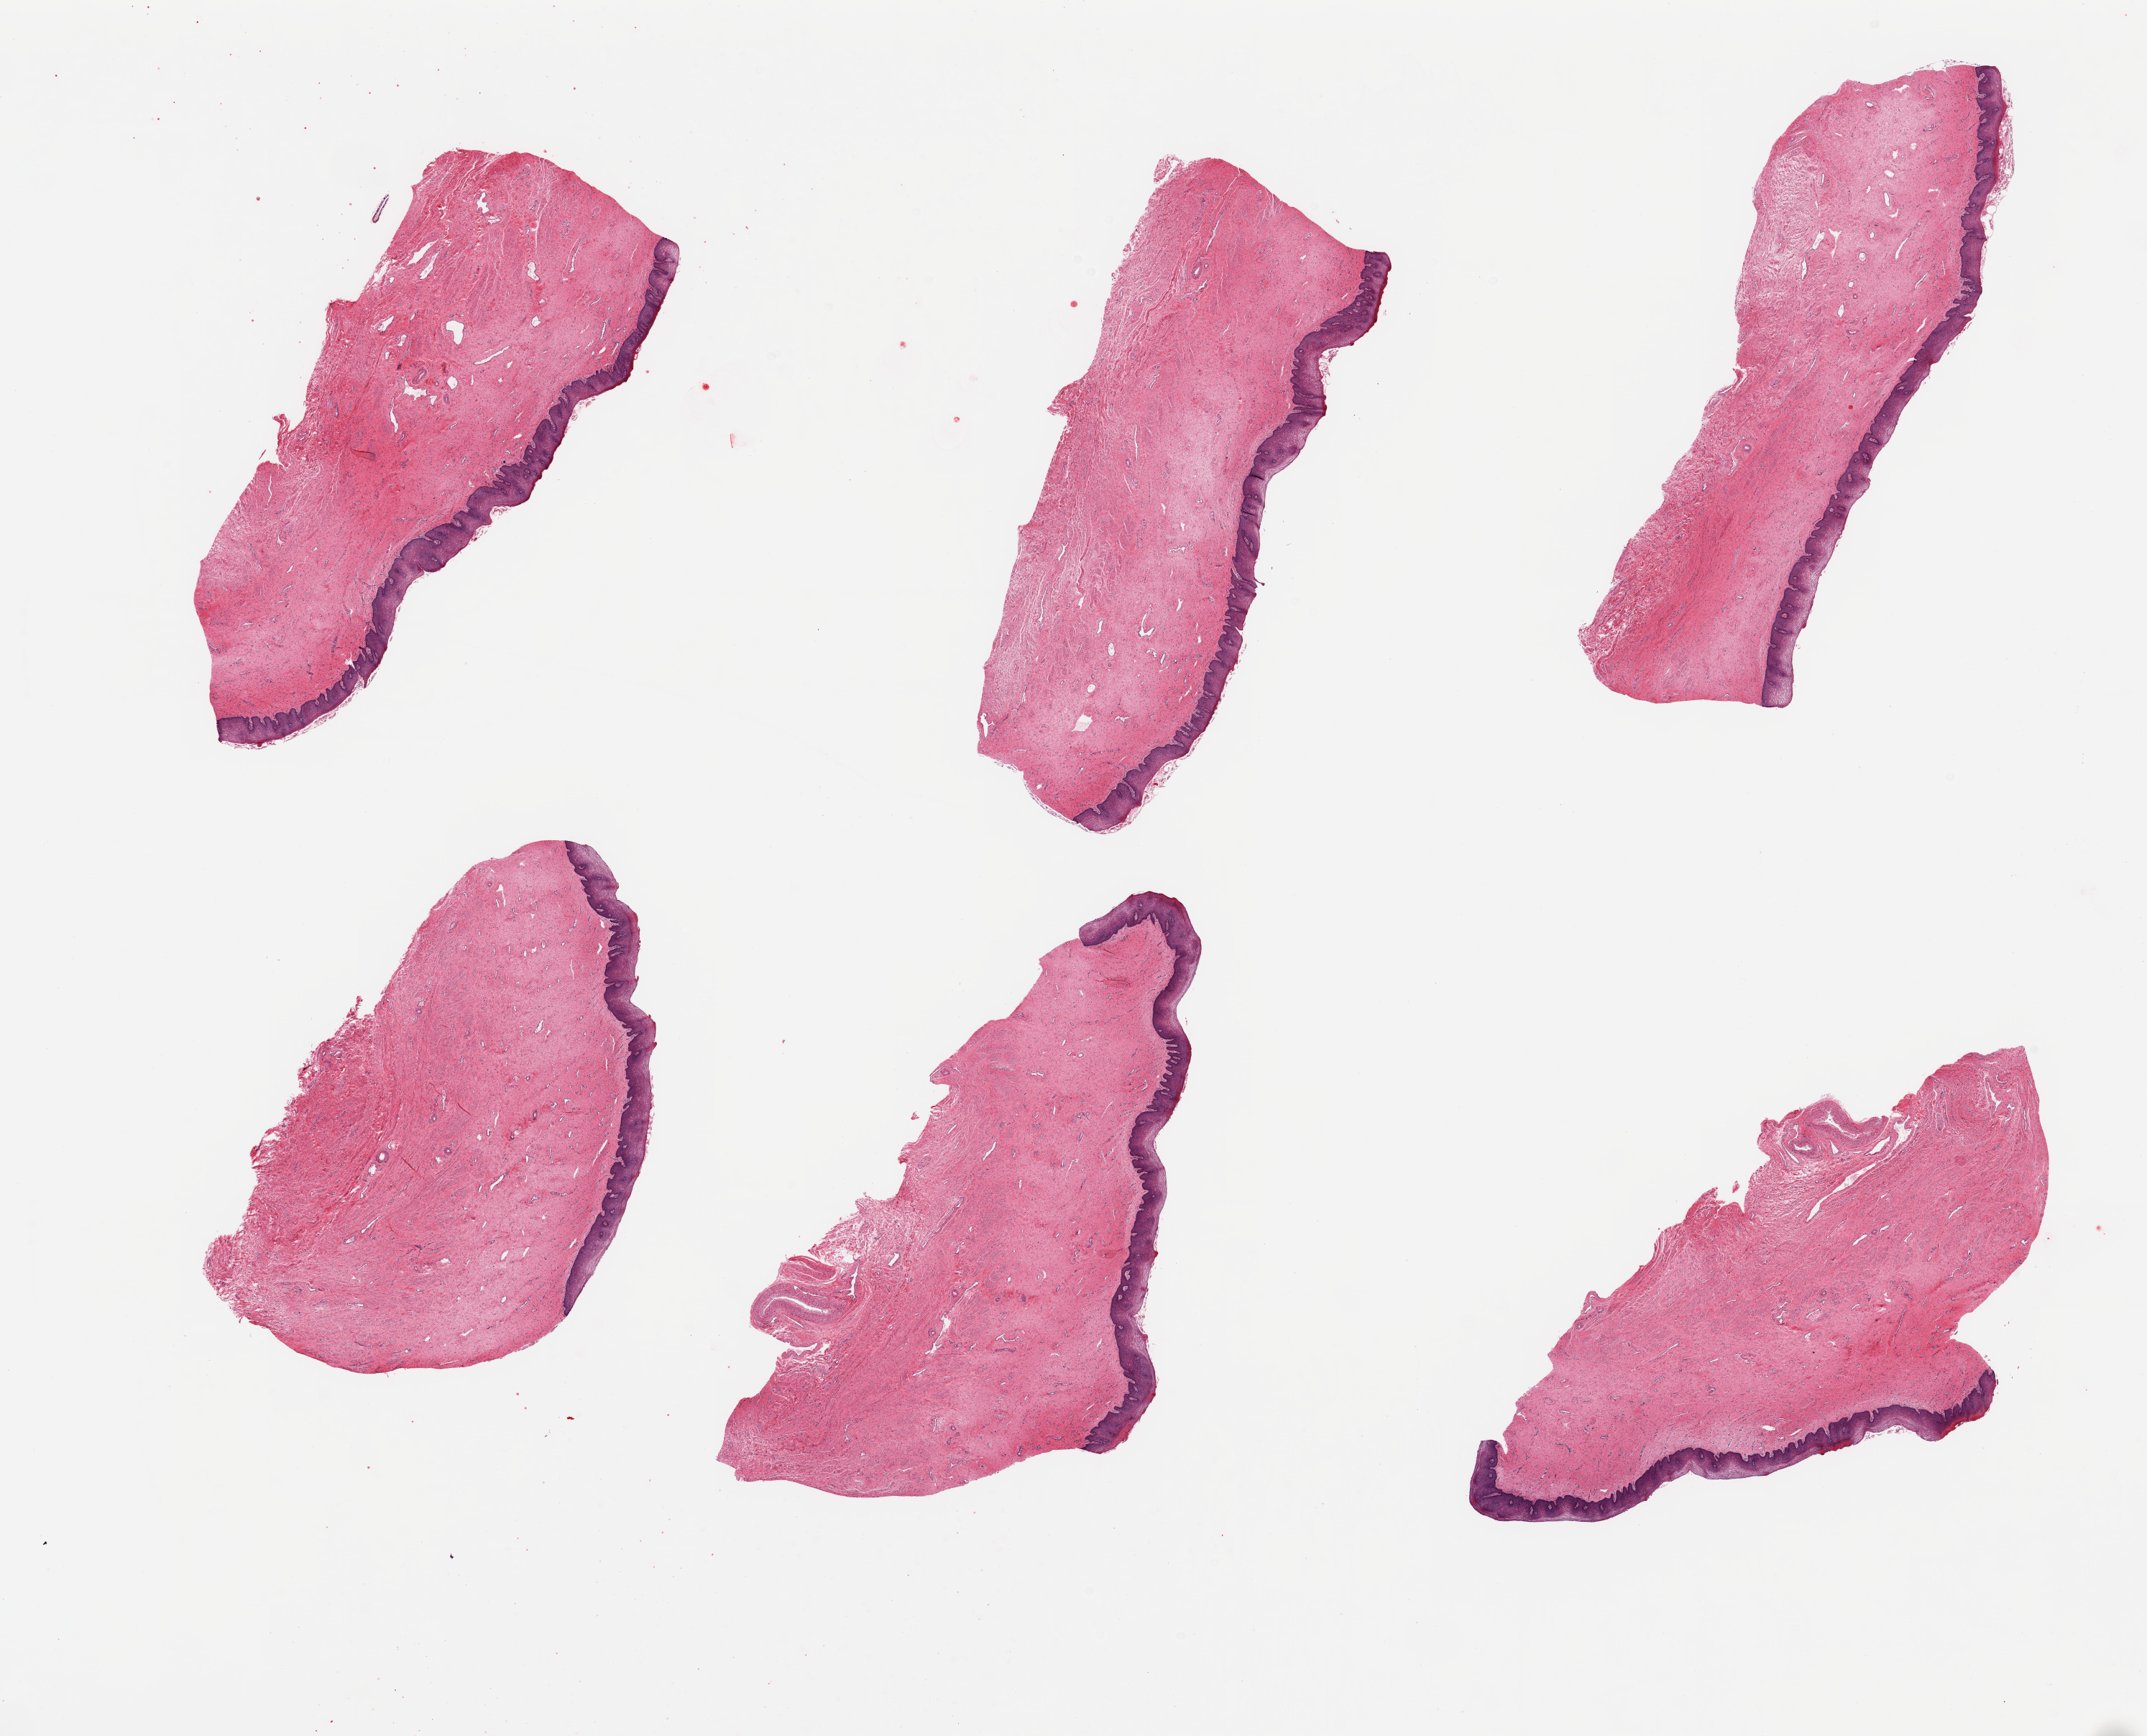
Whole-slide image, H&E stain, brightfield — low-resolution overview of the scanned area, about 23.6 x 19.1 mm (from a 20x scan), PAXgene-fixed, paraffin-embedded tissue, target tissue: vagina, donor tissue sample. Donor: female.
- review note (as recorded): 6 pieces; focal epithelial sloughing